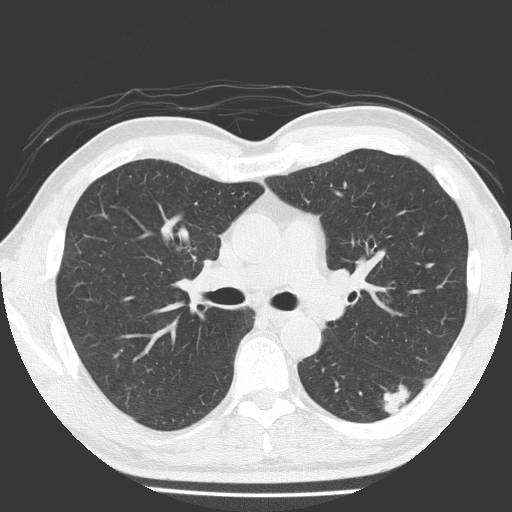
Axial slice from a low-dose chest CT screening exam. Baseline annual screen. Lung window (W 1500 / L -600 HU). 2 mm slice thickness. Lung (sharp) reconstruction kernel (FC51). 512 × 512 image matrix, field of view 348 × 348 mm. Male participant, aged 58 years at enrolment. Current smoker at enrolment.
Expert reader's lesion annotation, bounding box [x1, y1, x2, y2] px = [372, 374, 425, 422]. The screening reader recorded 4 non-calcified nodules or masses ≥4 mm on this exam (left lower lobe, left lower lobe, right middle lobe, left upper lobe); which of them this box marks is not recorded. Participant outcome: lung cancer diagnosed 99 days after this screen — adenosquamous carcinoma, left lower lobe, moderately differentiated (G2), stage IA (AJCC 6th edition), 28 mm at pathology.